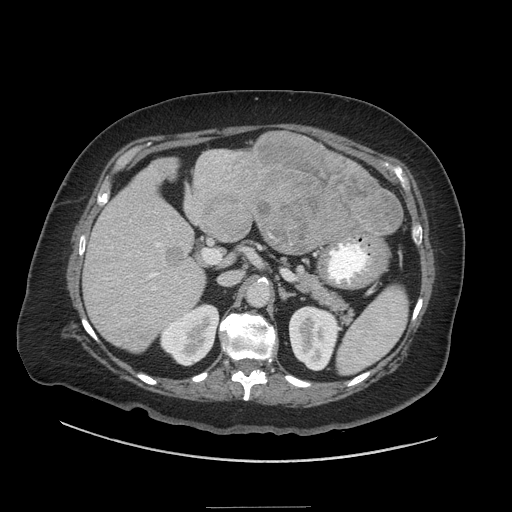
Contrast-enhanced abdominal CT (liver protocol), one axial slice. Slice 20 of 81 in the series (ordered by position). Reconstruction kernel STANDARD. 140 kVp. Soft-tissue window (W 400 / L 40 HU). 2.5 mm slice thickness. 512 × 512 image matrix, field of view 440 × 440 mm. Case-level facts recorded for this patient, not image findings: diagnosis: hepatocellular carcinoma (patient treated with transarterial chemoembolisation; whether this scan precedes or follows treatment is not stated here); TNM stage (as recorded): Stage-II; Child-Pugh class: A; tumour differentiation: moderately differentiated; tumour nodularity: multinodular.
Structures marked on this image (semi-automatic segmentation, software-assisted and operator-edited):
- liver parenchyma outside the tumour (the mass and vessels are separate outlines, so this box may not span the whole liver): bounding box <82,146,402,352> (left, top, right, bottom; pixels)
- mass: <137,130,403,341>
- liver vessels: <106,227,190,293>